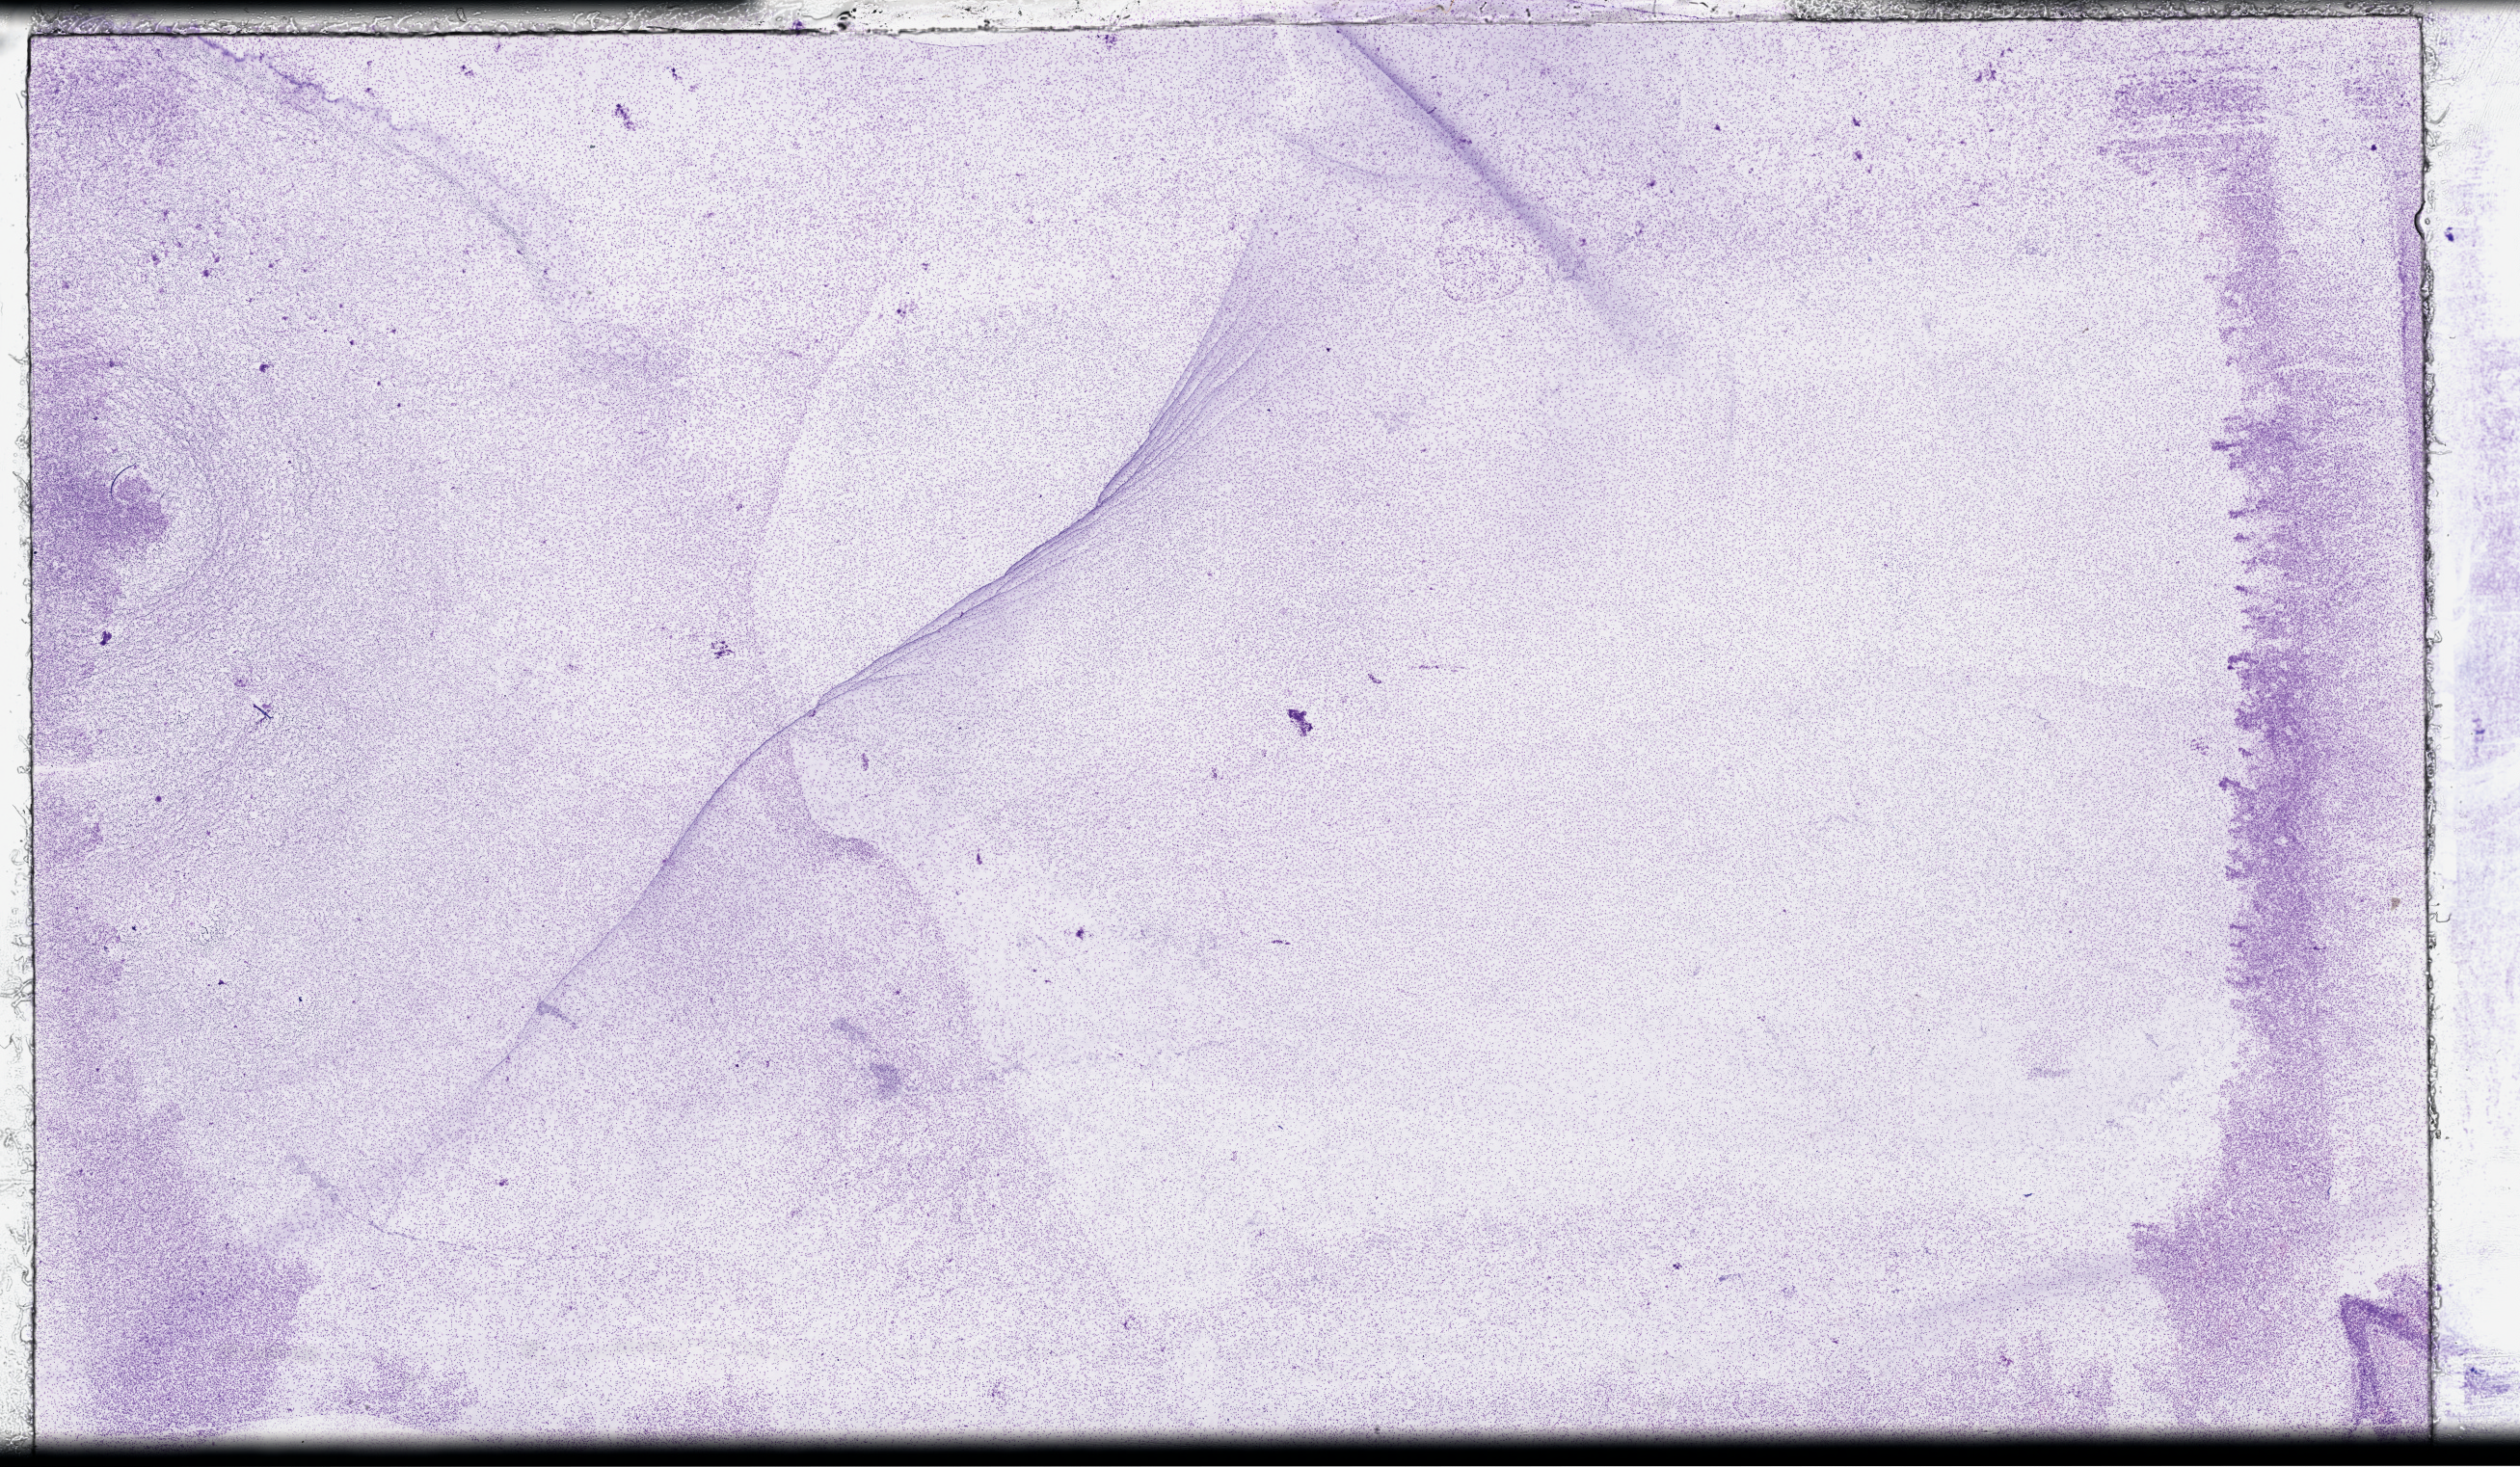
Whole-slide histology image, H&E-stained — low-resolution overview of the scanned area, about 42.2 x 24.6 mm (acquisition: 40x scan), peripheral blood (leukaemic) sample. Patient: female, age 47 years.
* diagnosis: Acute Myeloid Leukemia
* WHO classification: AML with maturation
* FAB classification: M2